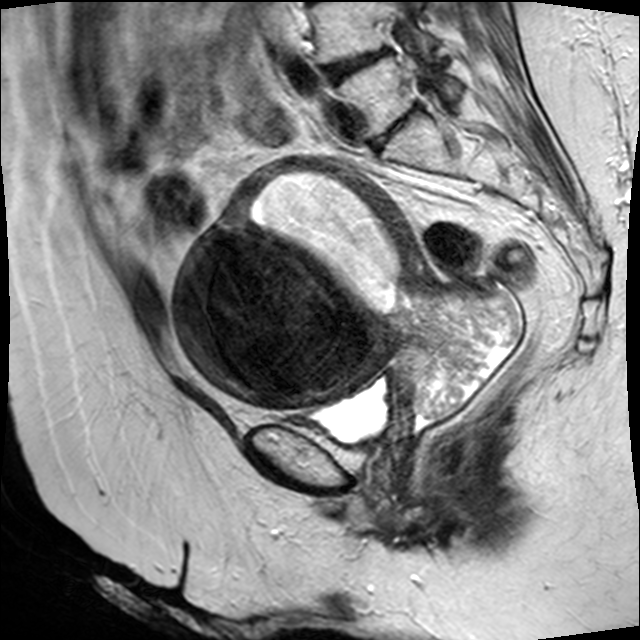
Pelvic MRI for cervical cancer, one sagittal slice; position 21 of 45 along the scan axis; T2-weighted; 1.5 T; TE 89 ms, TR 4610 ms; 4 mm slice thickness; 640 × 640 image matrix, field of view 260 × 260 mm. Patient: female, 50 years.
Outlined on this slice (outlined manually by an expert reader):
- uterus and cervix: bounding box (x1, y1, x2, y2) in pixels: (173, 154, 522, 419)